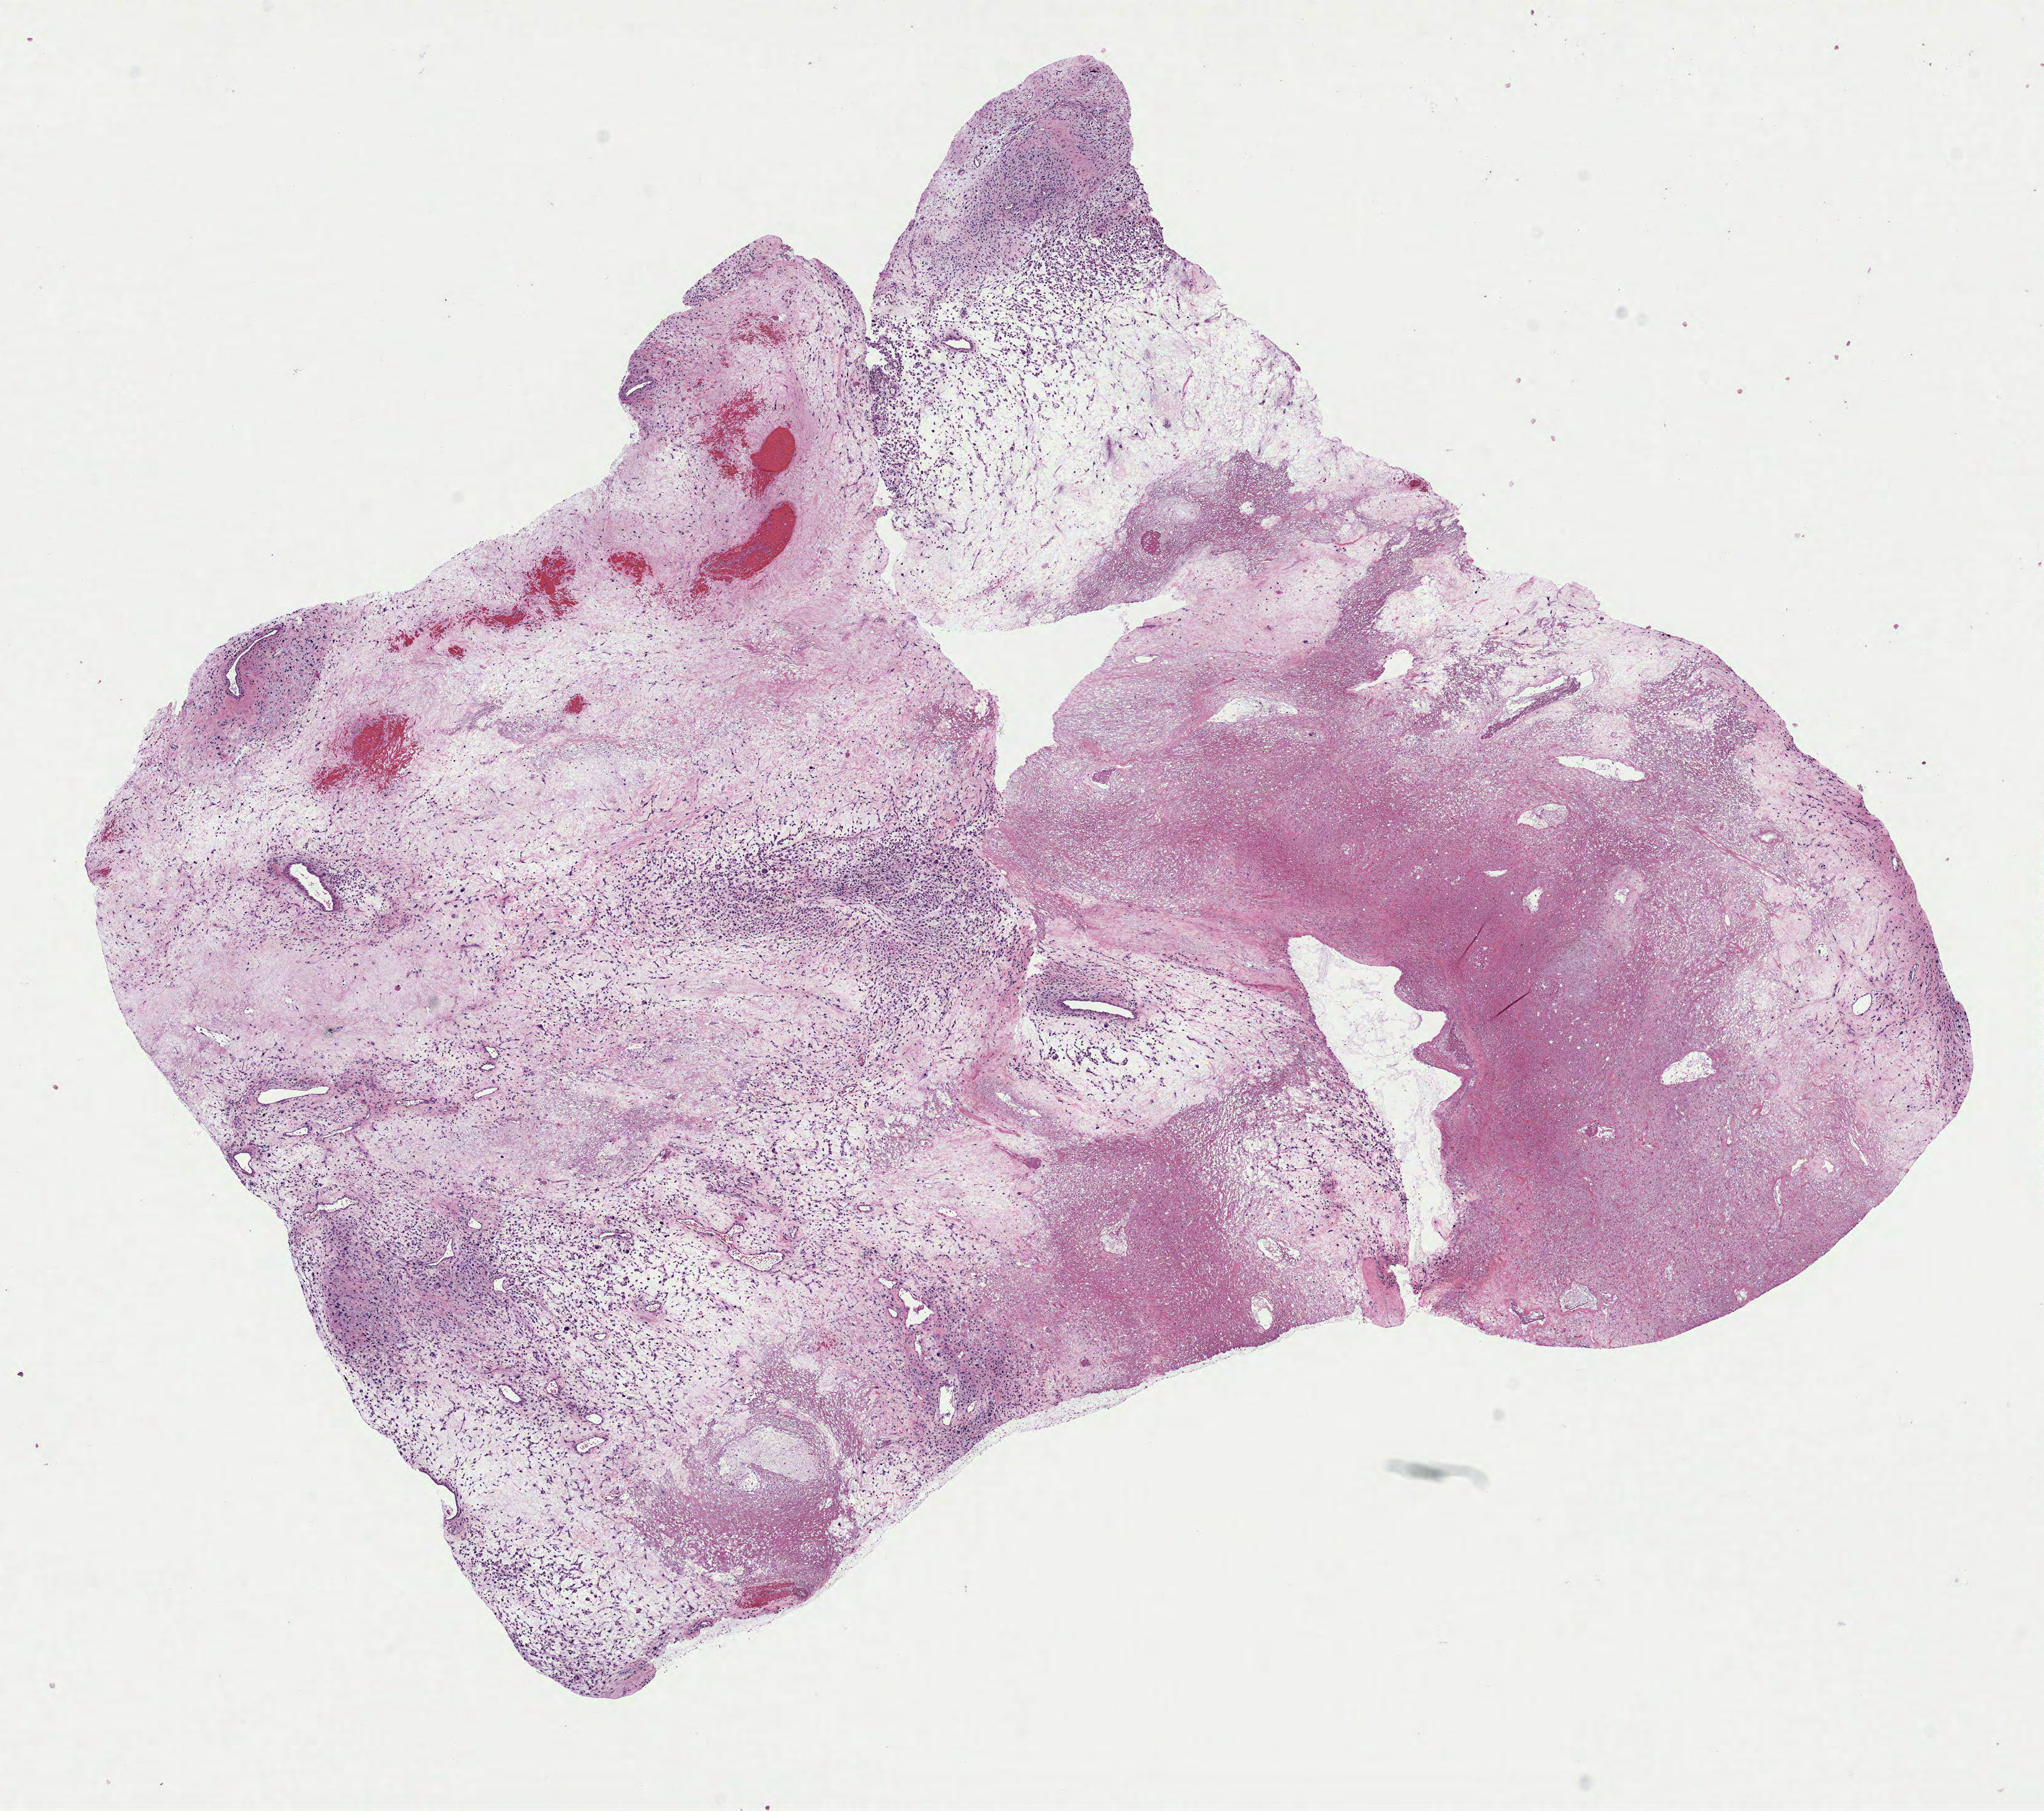
Whole-slide histology image, H&E-stained — whole scanned area (about 13.3 x 11.8 mm, from a 40x scan) shown as a low-resolution overview, formalin-fixed paraffin-embedded (FFPE) diagnostic section, retroperitoneum and peritoneum, primary tumour sample. Patient: male, age at initial diagnosis 87 years.
Pathologic diagnosis: Malignant fibrous histiocytoma (retroperitoneum).